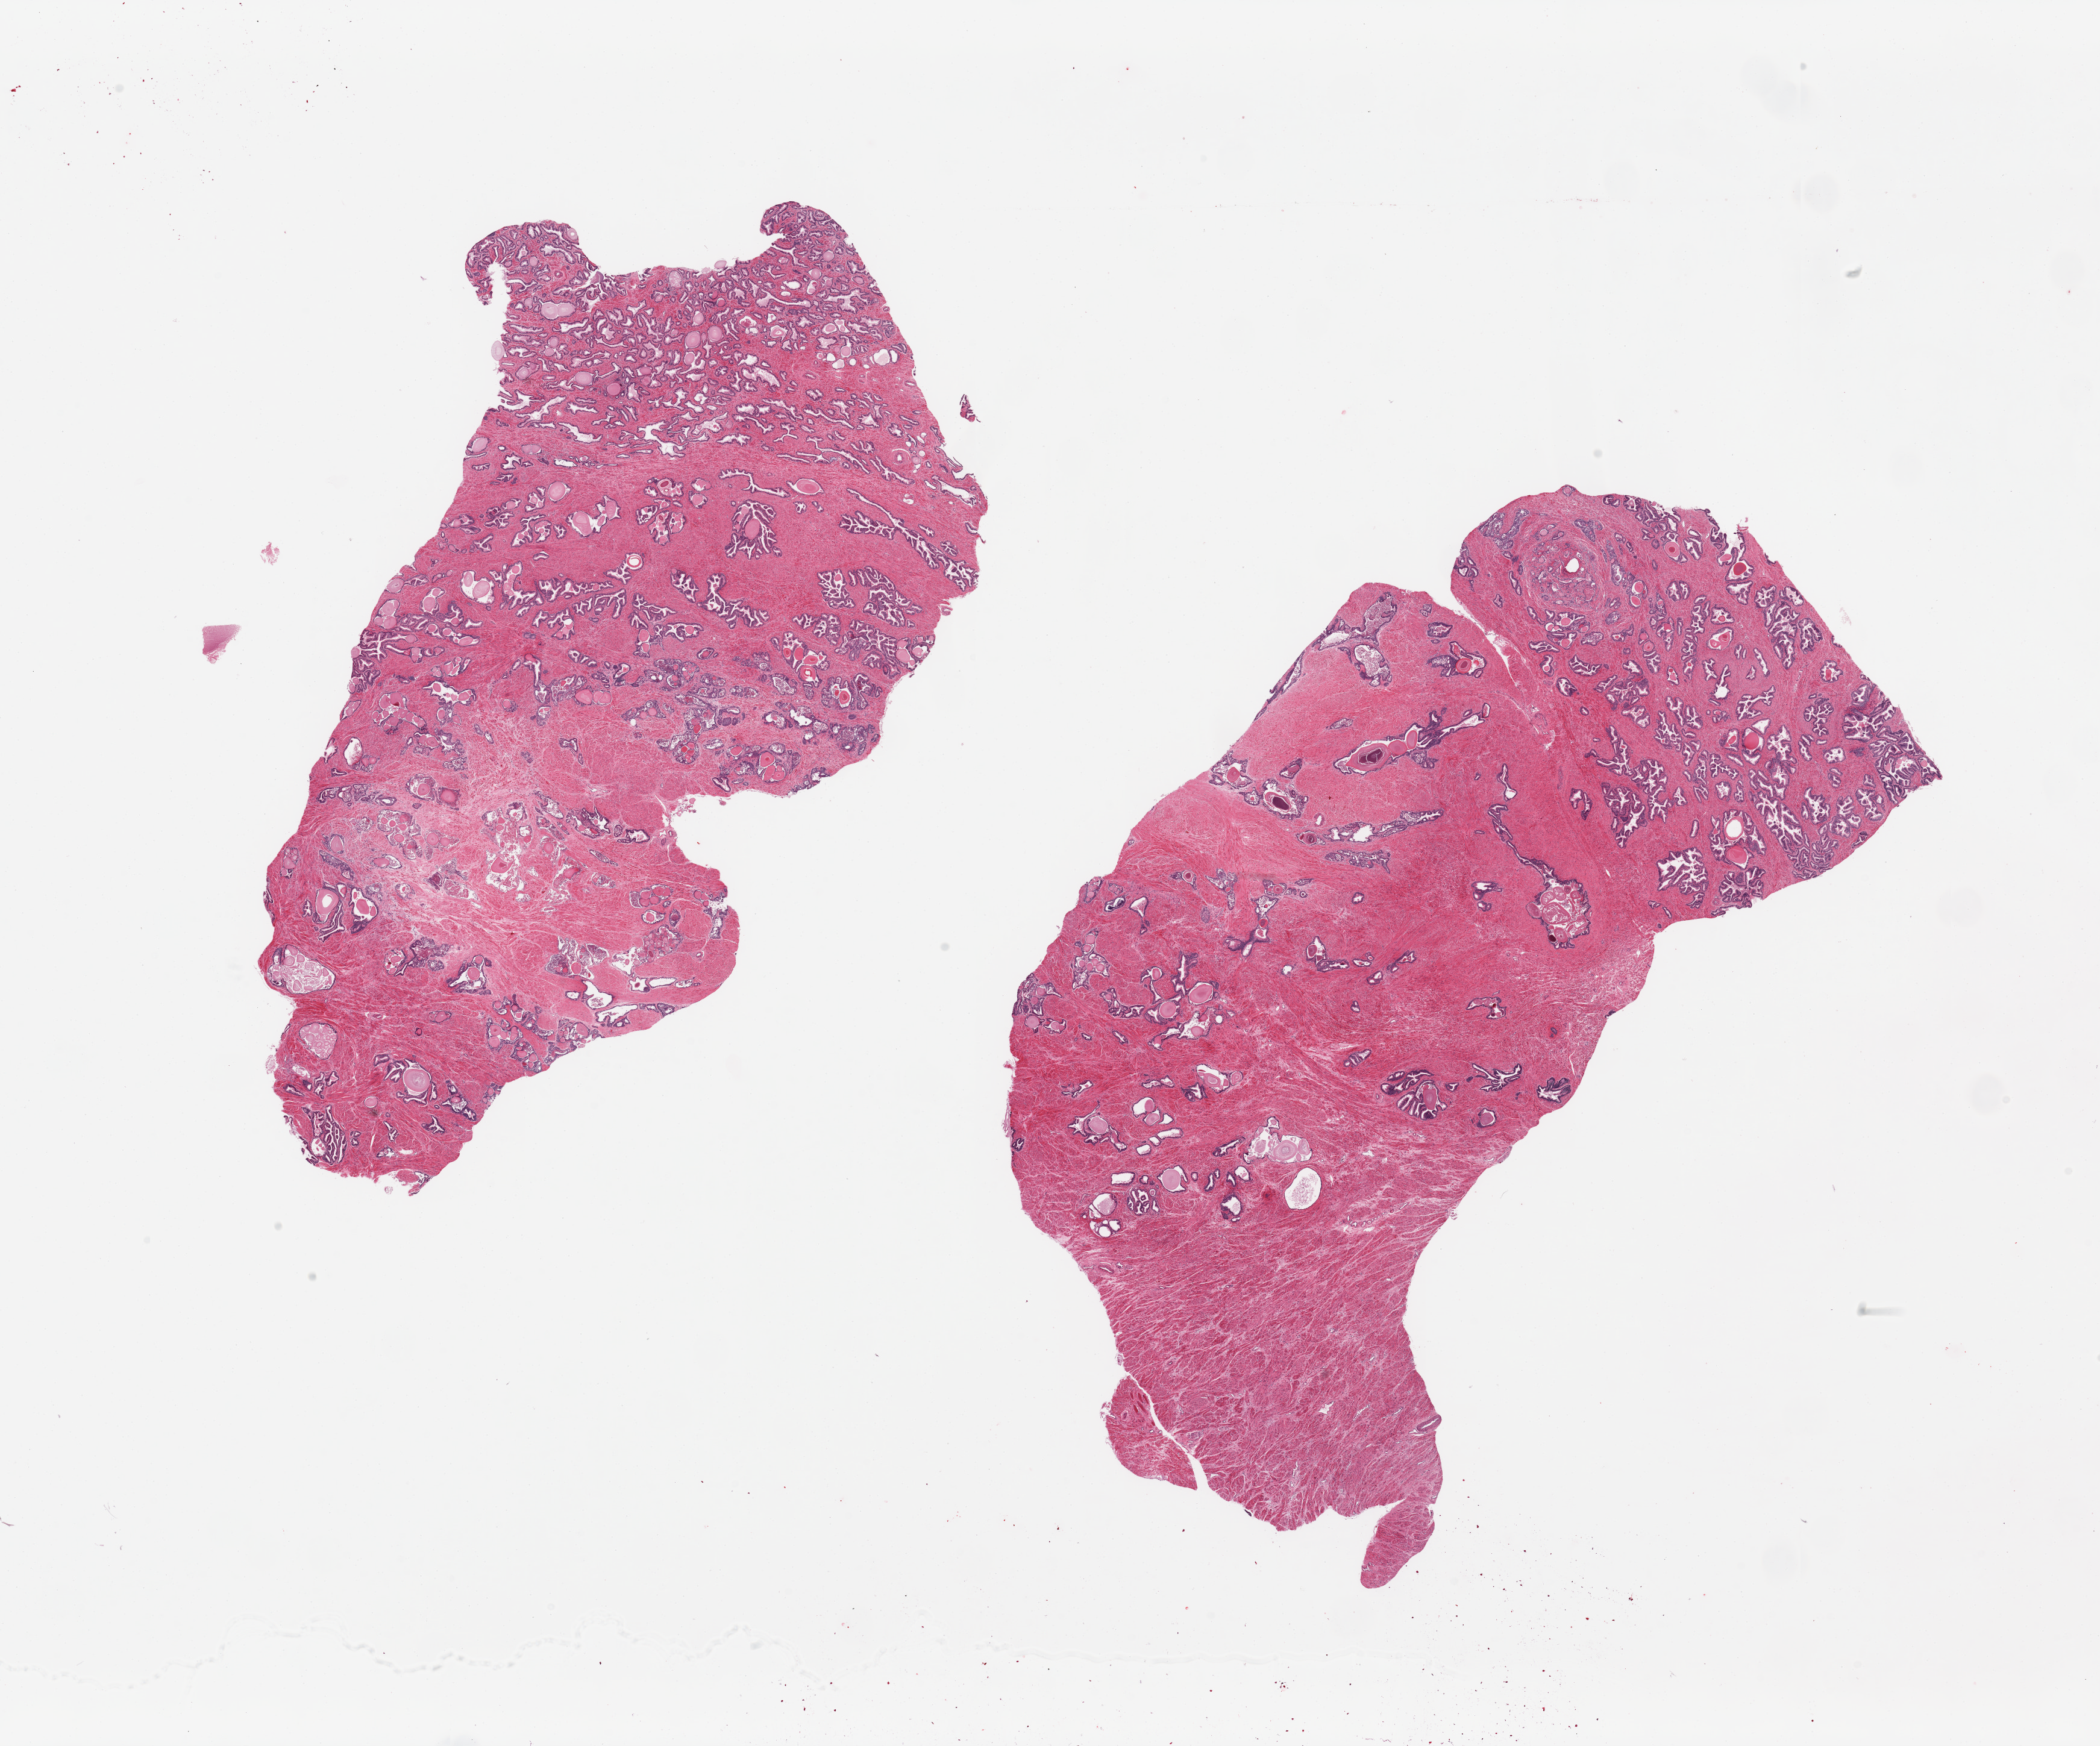
Whole-slide image, haematoxylin and eosin stain, low-resolution overview of the scanned area, about 27.6 x 22.9 mm (slide scanned at 20x); PAXgene-fixed, paraffin-embedded tissue; target tissue: prostate; tissue donor sample.
Review note (as recorded): 2 pieces; prostatitis.